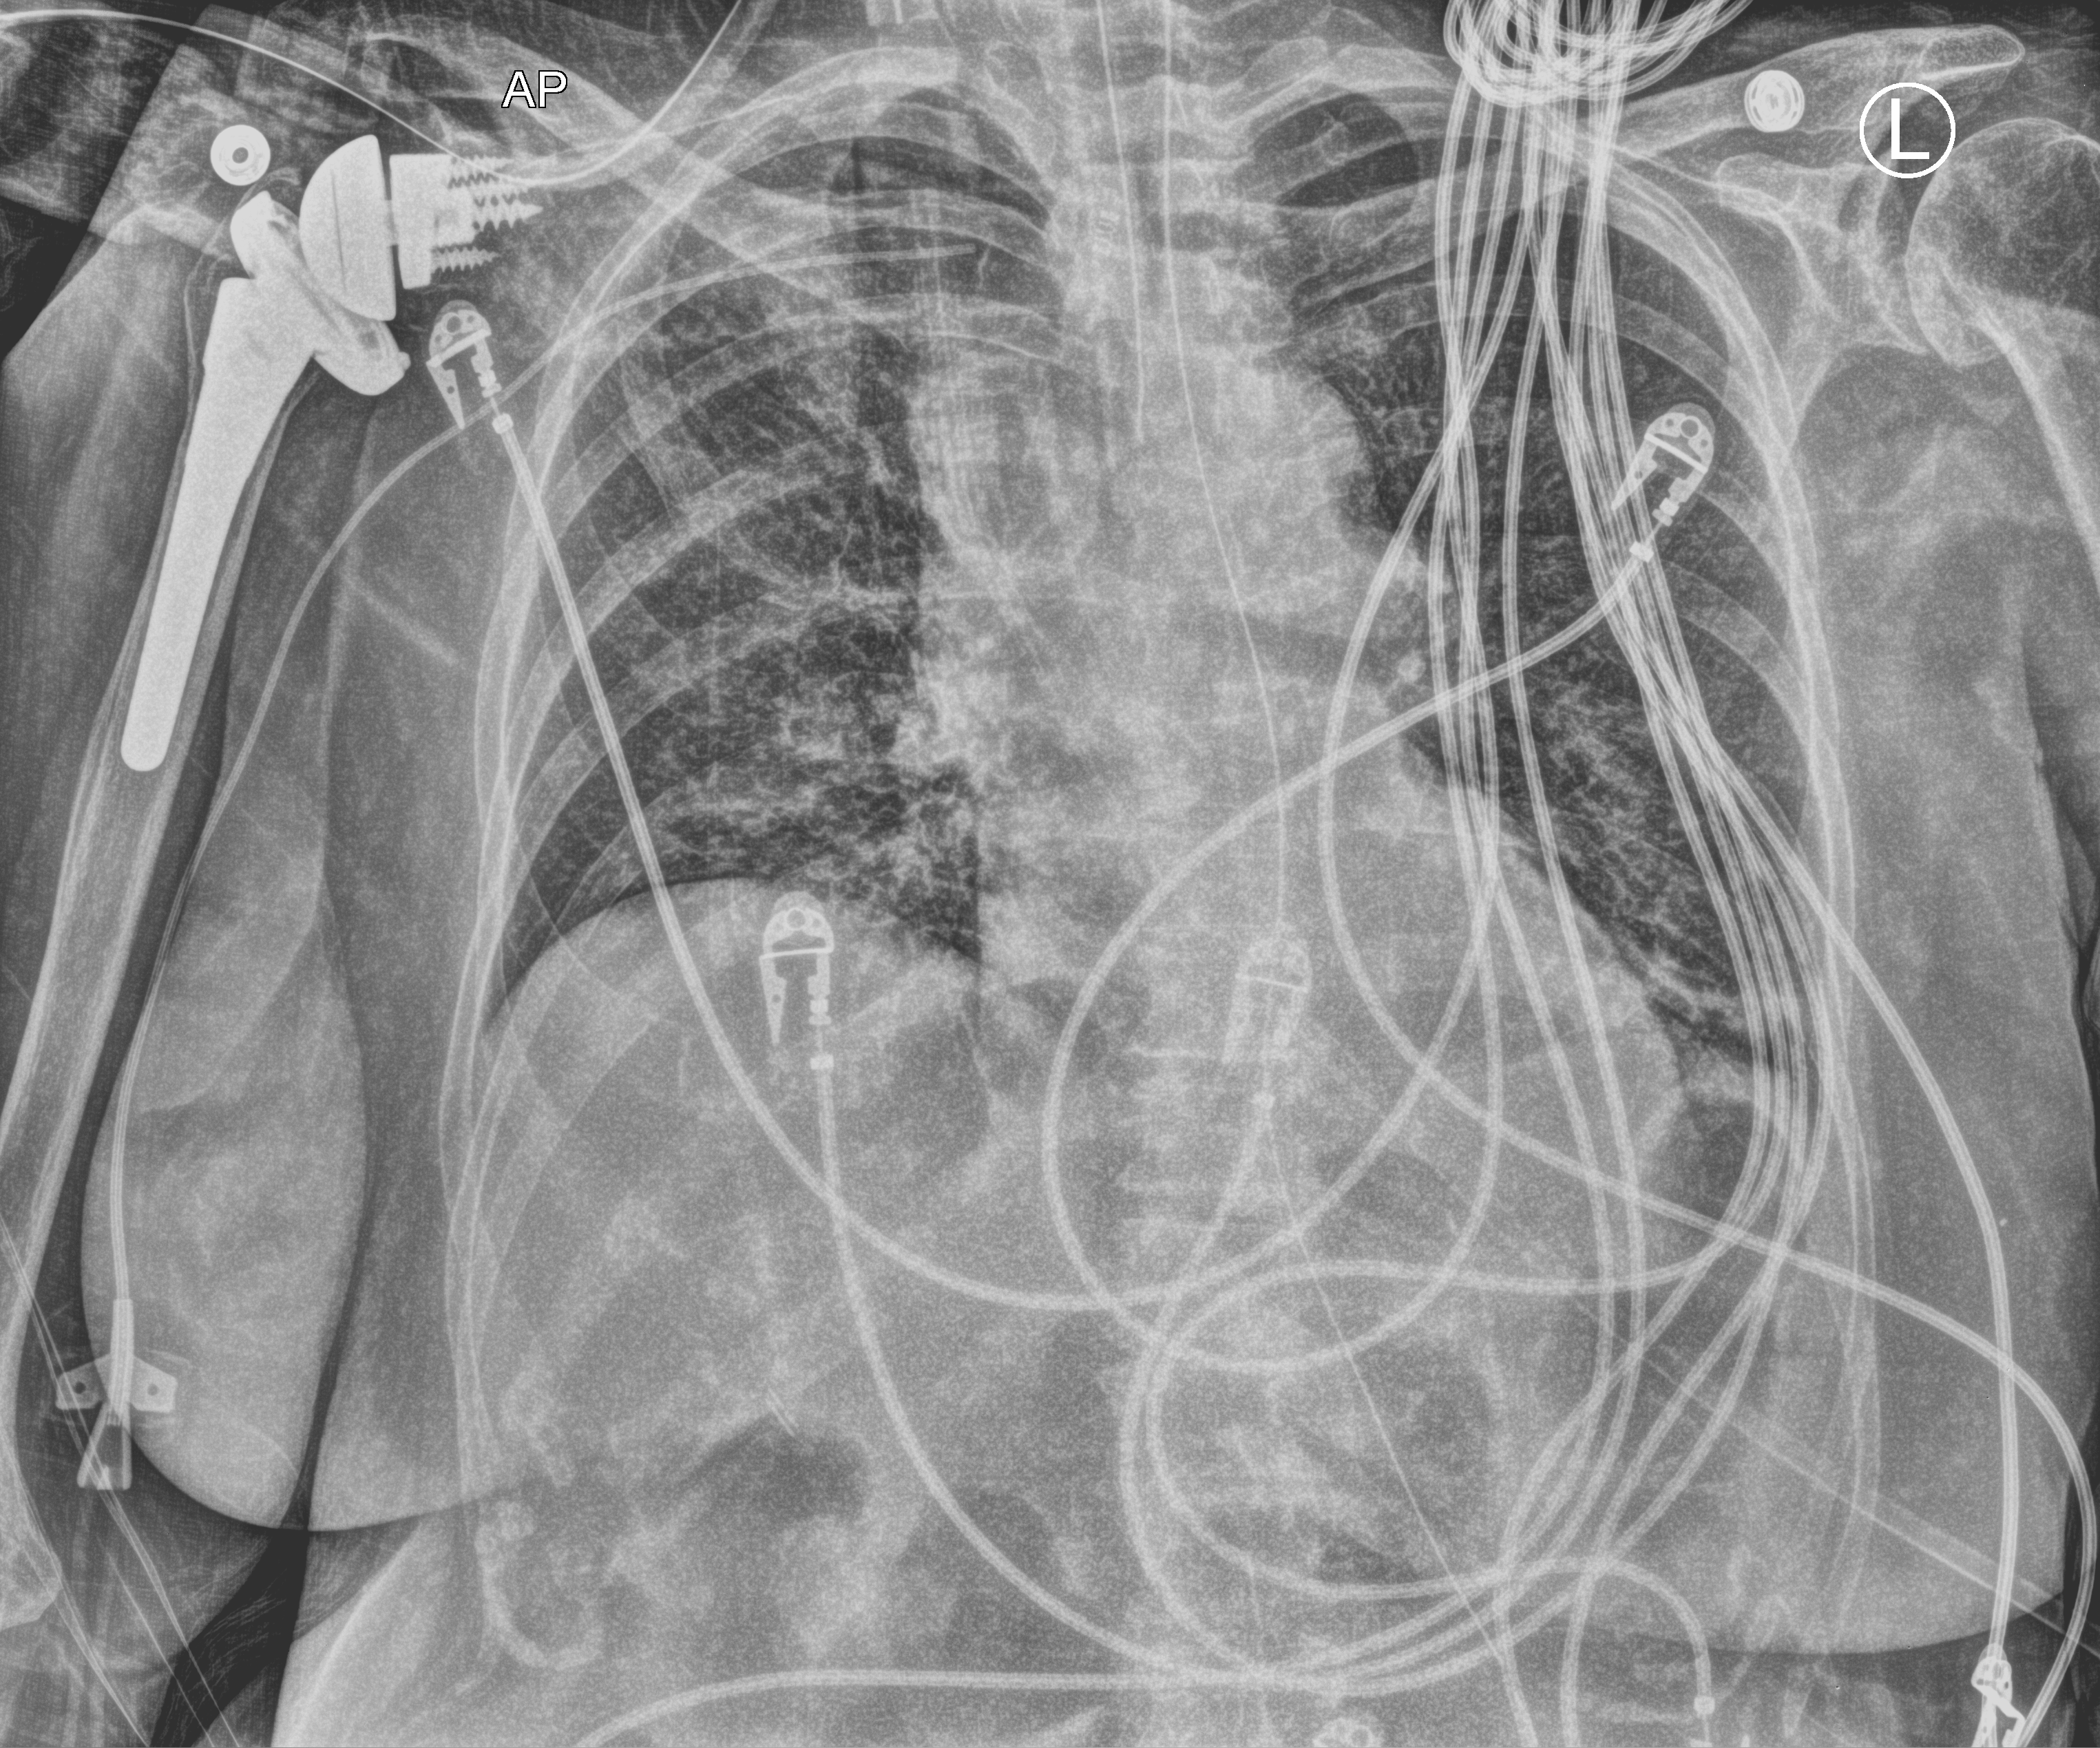
Bedside chest radiograph (computed radiography), anteroposterior (AP) projection. Female patient hospitalised with COVID-19, age 60–74 years.
From the hospital-stay record, not from the radiograph (when in the stay this image was taken is not recorded): admitted to intensive care during this hospital stay: yes; mechanically ventilated during this hospital stay: yes.